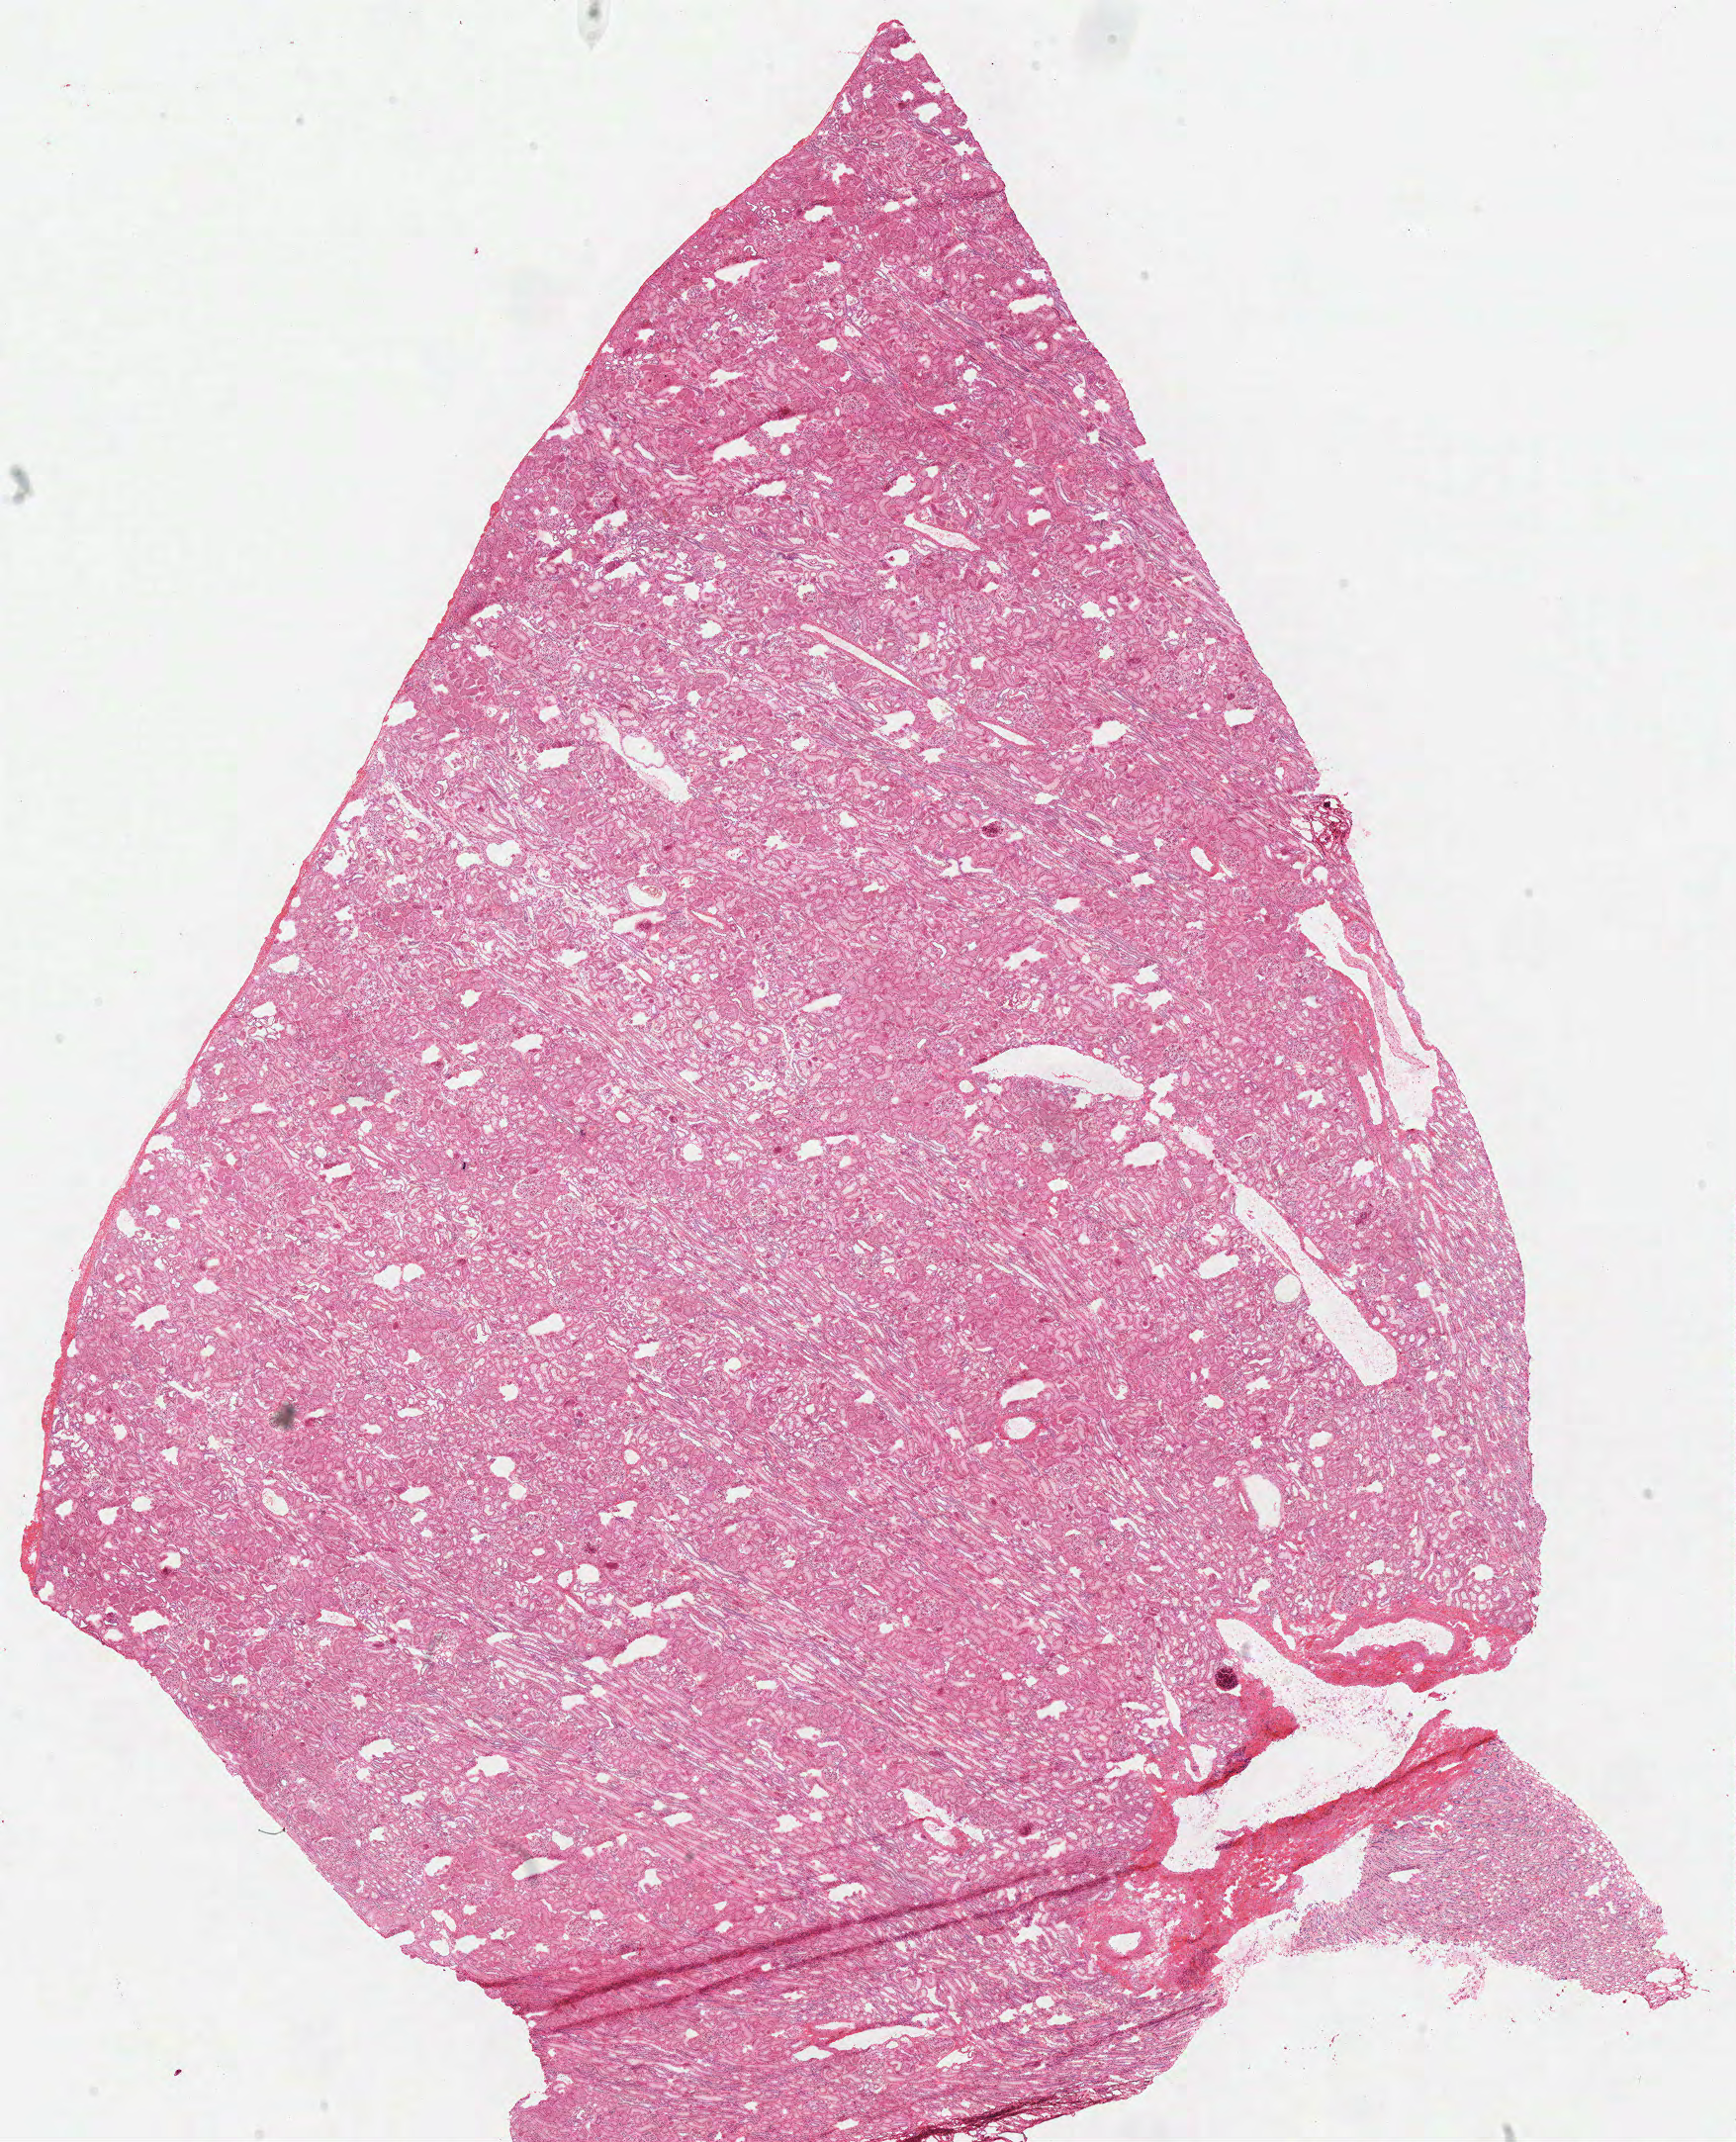
Digitized H&E-stained tissue section (whole slide) — low-resolution overview of the scanned area, about 13.8 x 17.1 mm; frozen section from the top of the tissue portion; sample: solid tissue normal (non-tumour tissue), kidney. Patient: female, age at initial diagnosis 32 years.
This section: solid tissue normal sample (biorepository sample class). Patient diagnosis: Papillary adenocarcinoma, NOS.